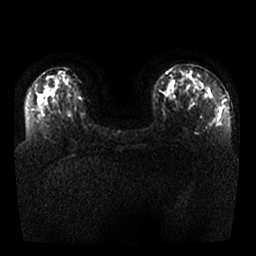
Breast MRI, one axial slice. Slice 12 of 25 in the series (ordered by position). Diffusion-weighted series; image 2 of 4 stored at this slice position (different b-values; order by instance number). 1.5 T. 256 × 256 image matrix, field of view 340 × 340 mm. Female patient.
Outlined on this slice (outlined manually by an expert reader):
- tumour on diffusion-weighted imaging: bounding box (x1, y1, x2, y2) in pixels: (182, 72, 214, 100)